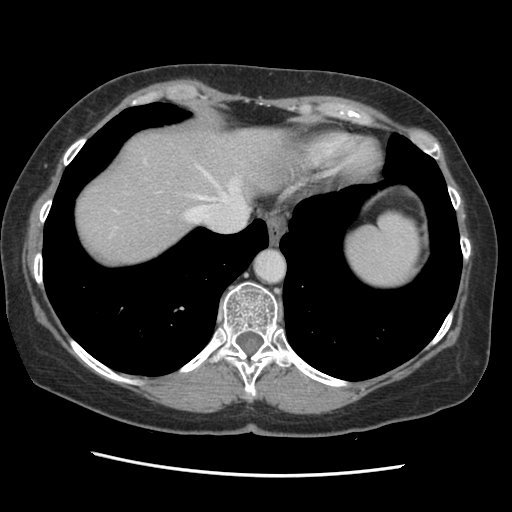
Contrast-enhanced abdominal CT, one axial slice; position 120 of 141 along the scan axis; 120 kVp; soft-tissue window (W 400 / L 40 HU); 2.5 mm slice thickness; 512 × 512 image matrix, field of view 330 × 330 mm. Female patient, age 61 years. From the clinical record (not read from this slice): diagnosis: colorectal cancer liver metastases, imaged before liver resection; multiple liver metastases: no; largest metastasis: 2.4 cm; disease in both lobes: no.
Structures marked on this image (expert manual segmentation):
- hepatic veins: bounding box (x1, y1, x2, y2) in pixels: (113, 166, 242, 222)
- liver: (74, 126, 294, 267)
- planned liver remnant (the part of the liver to remain after resection): (74, 126, 294, 267)